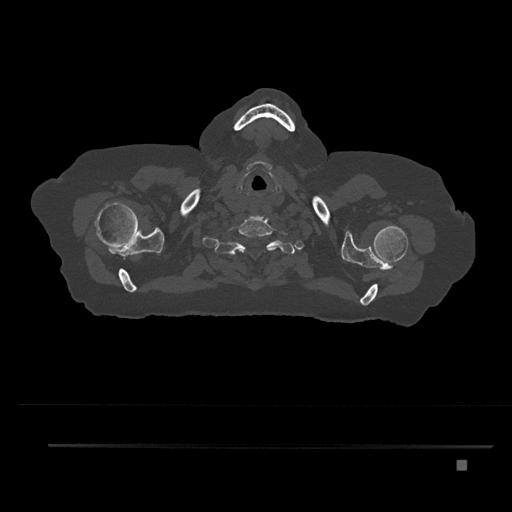
CT including the spine, one axial slice; slice 712 of 797 in the series (ordered by position); 120 kVp; bone window (W 1800 / L 400 HU); 512 × 512 image matrix, field of view 437 × 437 mm. Patient: female, 76 years. From the clinical record (not read from this slice): primary cancer: lung; vertebrae with lytic lesions (as recorded): T11, L3.
Structures marked on this image (semi-automatically segmented with operator editing):
- T1 vertebra: bounding box (x1, y1, x2, y2) in pixels: (223, 240, 286, 256)